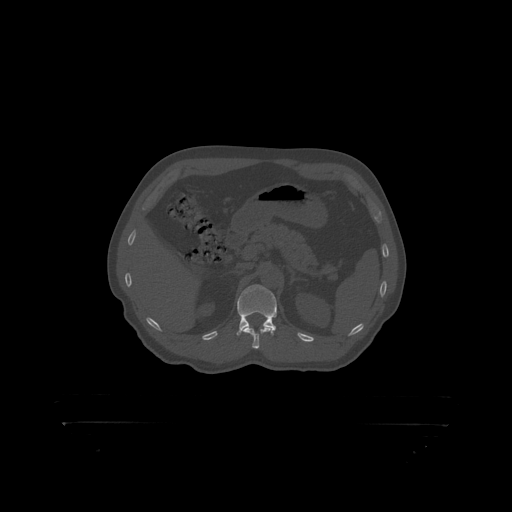
CT including the spine, one axial slice. Slice 337 of 399 in the series (ordered by position). 120 kVp. Bone window (W 1800 / L 400 HU). 1.25 mm slice thickness. 512 × 512 image matrix, field of view 650 × 650 mm. Patient: male, 46 years. From the clinical record (not read from this slice): primary cancer: skin.
Structures marked on this image (semi-automatically segmented with operator editing):
- L1 vertebra: bounding box <238,285,277,318> (left, top, right, bottom; pixels)